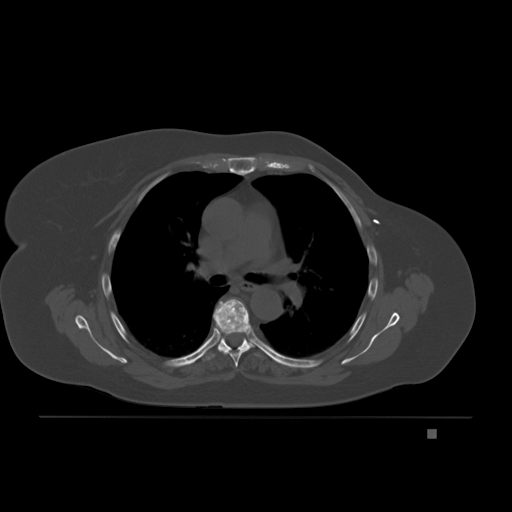
CT including the spine, one axial slice. Position 141 of 221 along the scan axis. Bone window (W 1800 / L 400 HU). 512 × 512 image matrix, field of view 474 × 474 mm. Female patient, age 63 years. Case-level facts recorded for this patient, not image findings: primary cancer: breast.
Outlined on this slice (semi-automatic segmentation, software-assisted and operator-edited):
- T5 vertebra: bounding box <211,299,259,368> (left, top, right, bottom; pixels)
- T6 vertebra: <206,314,250,360>